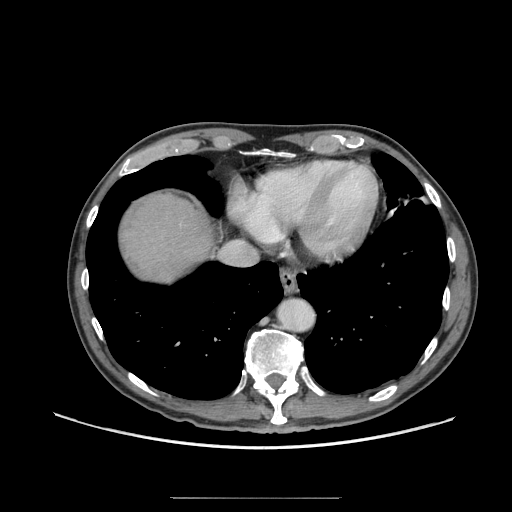
Contrast-enhanced abdominal CT (liver protocol), one axial slice. Slice 63 of 71 in the series (ordered by position). Reconstruction kernel STANDARD. 140 kVp. Soft-tissue window (W 400 / L 40 HU). 512 × 512 image matrix, field of view 400 × 400 mm. From the clinical record (not read from this slice): diagnosis: hepatocellular carcinoma (patient treated with transarterial chemoembolisation; whether this scan precedes or follows treatment is not stated here); TNM stage (as recorded): Stage-I; Child-Pugh class: A; tumour nodularity: uninodular; tumour size: 3.5 cm.
Outlined on this slice (semi-automatic segmentation, software-assisted and operator-edited):
- abdominal aorta: bounding box [x1, y1, x2, y2] px = [278, 299, 313, 332]
- liver parenchyma outside the tumour (the mass and vessels are separate outlines, so this box may not span the whole liver): [120, 194, 214, 282]